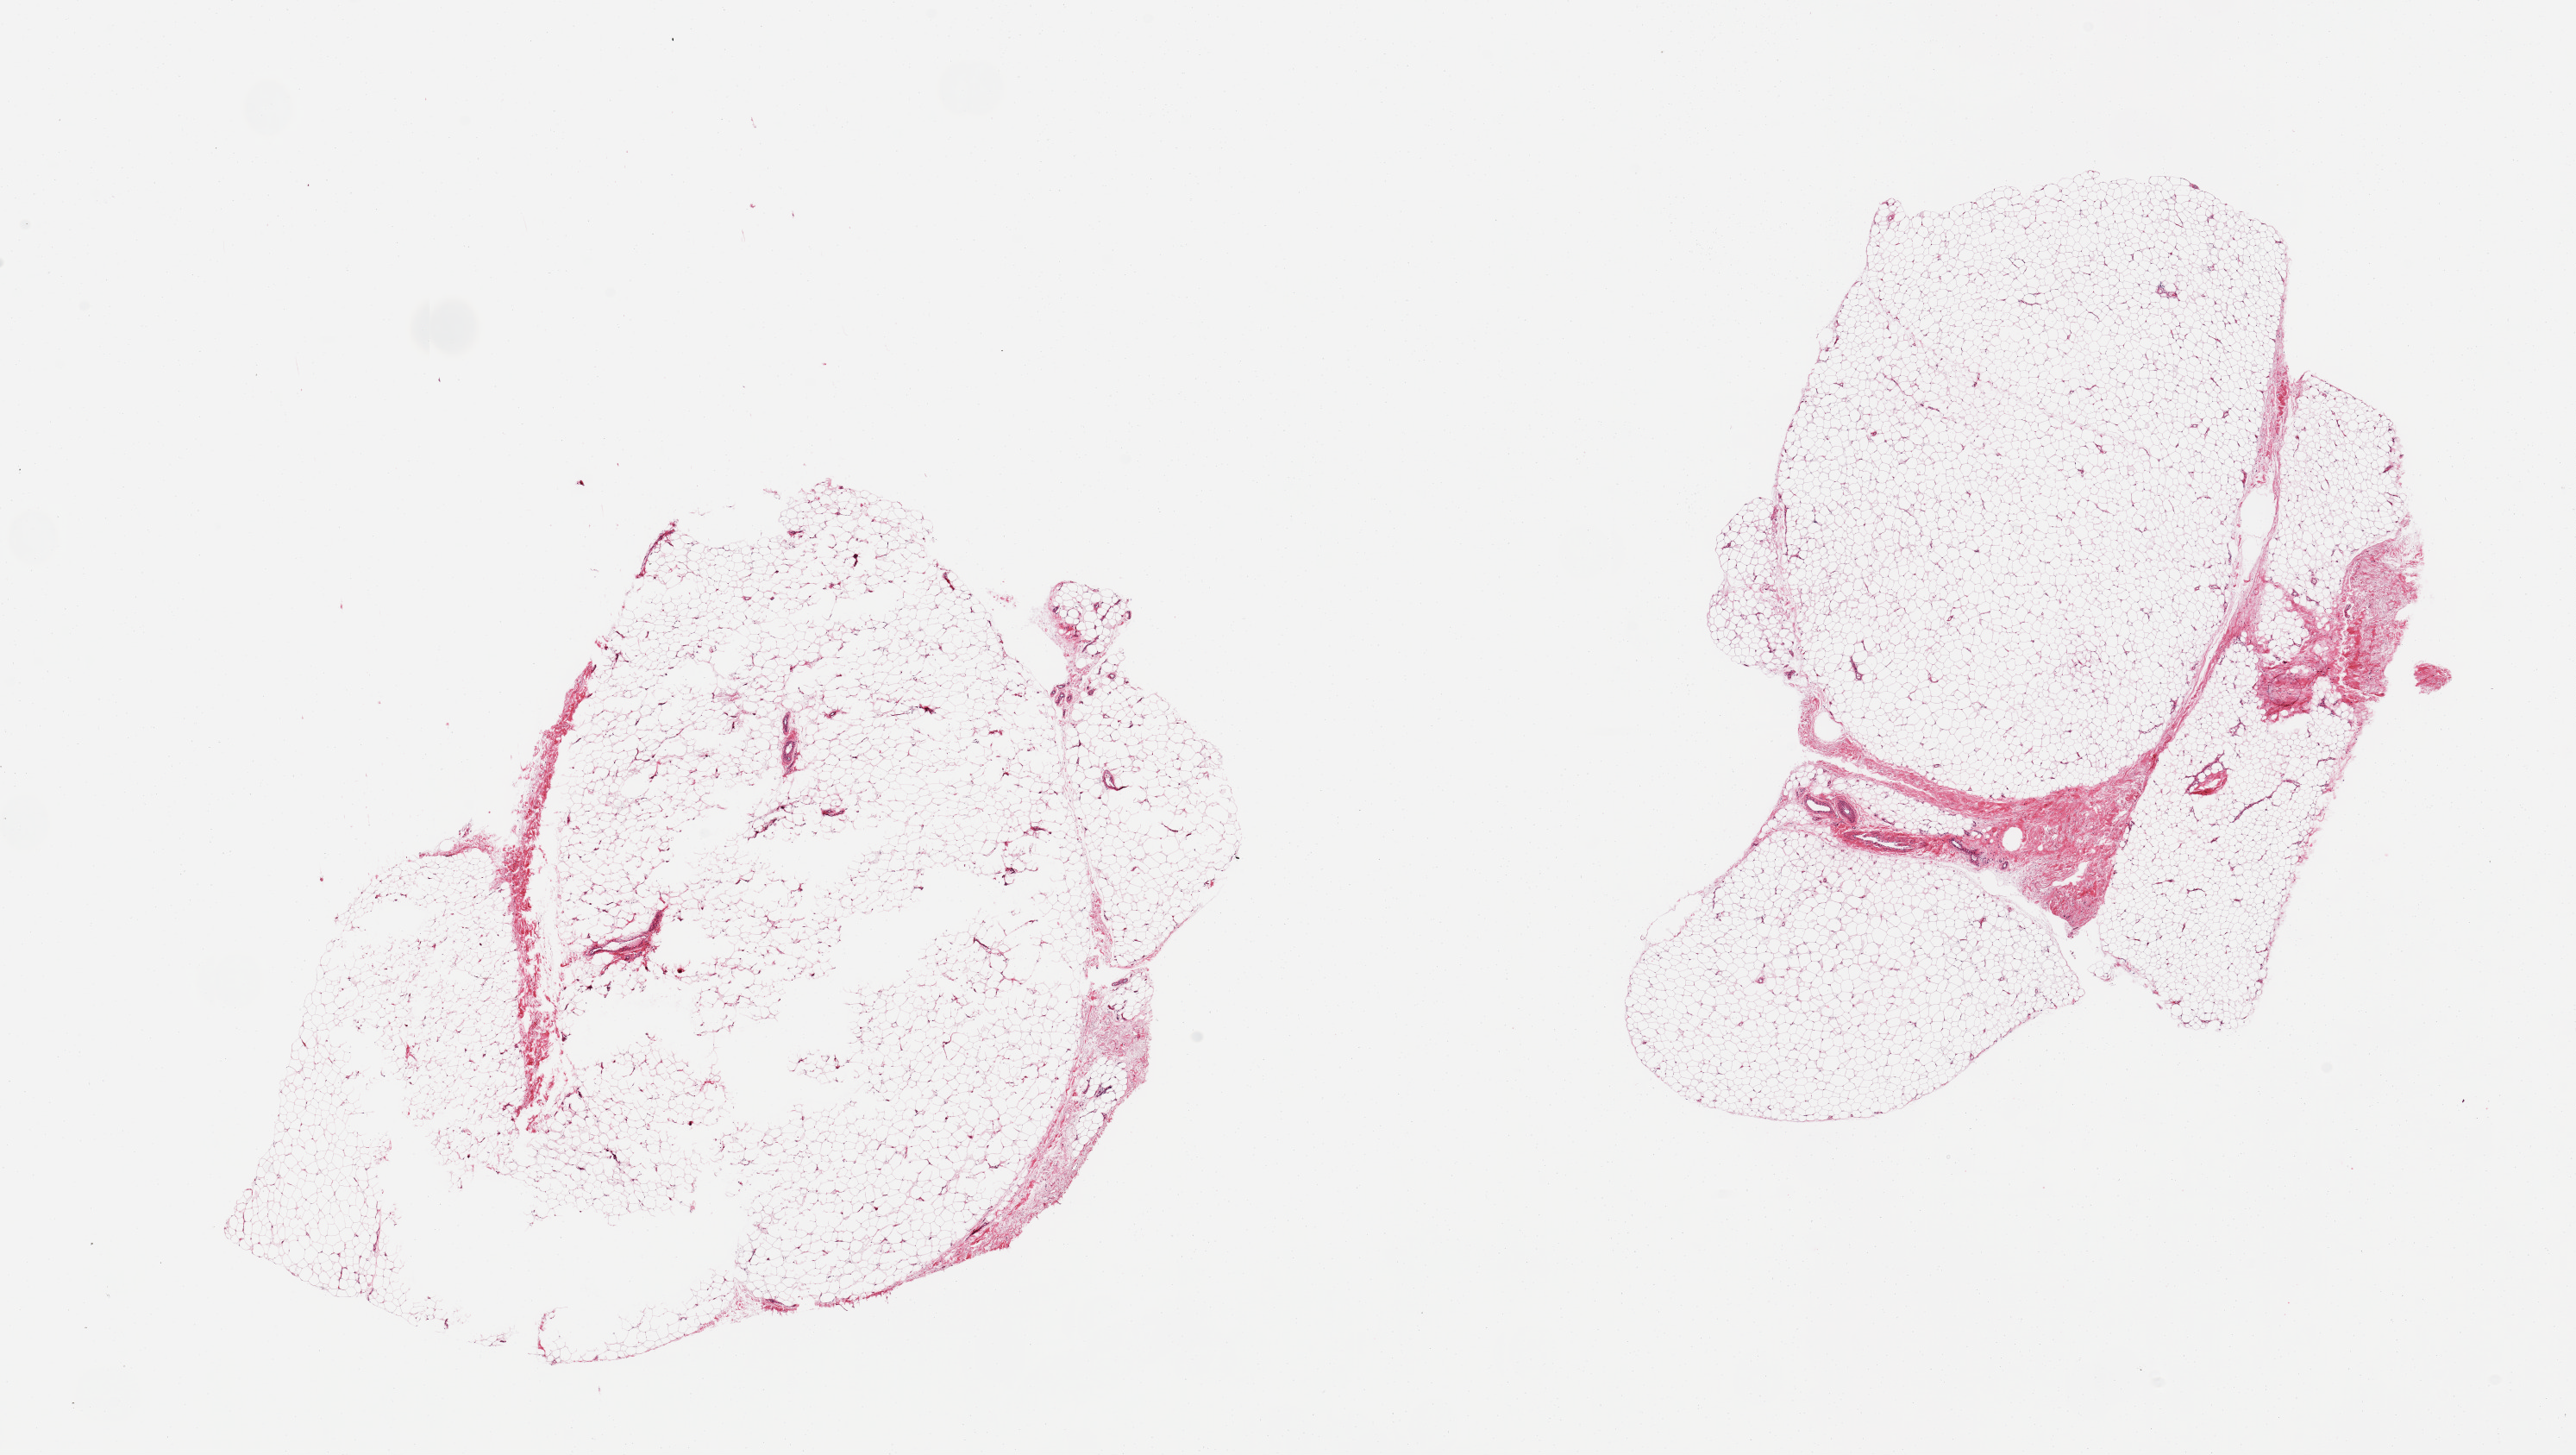
Digitized haematoxylin and eosin-stained section — shown as a low-resolution overview of the whole scanned area (about 23.6 x 13.3 mm, slide scanned at 20x), PAXgene-fixed paraffin-embedded (PFPE) section, section of adipose tissue (target tissue), tissue donor sample. Male donor.
* review note (as recorded): 2 pieces; several tissue holes; 5 & 10% fibrous content